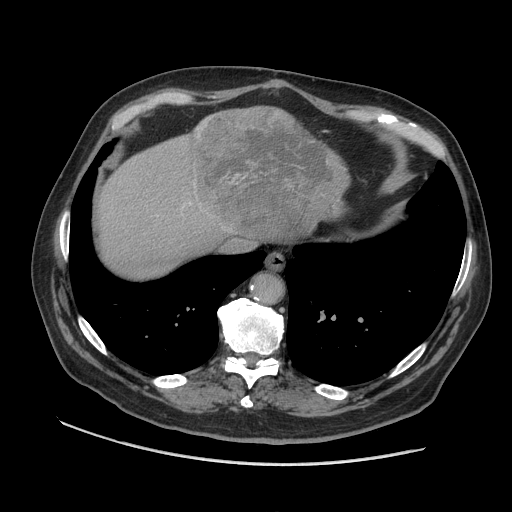
Contrast-enhanced abdominal CT (liver protocol), one axial slice. Position 86 of 109 along the scan axis. Reconstruction kernel STANDARD. 140 kVp. Soft-tissue window (W 400 / L 40 HU). 2.5 mm slice thickness. 512 × 512 image matrix, field of view 420 × 420 mm. Case-level facts recorded for this patient, not image findings: diagnosis: hepatocellular carcinoma (patient treated with transarterial chemoembolisation; whether this scan precedes or follows treatment is not stated here); TNM stage (as recorded): Stage-I; Child-Pugh class: A; tumour nodularity: uninodular.
Outlined on this slice (semi-automatically segmented with operator editing):
- liver parenchyma outside the tumour (the mass and vessels are separate outlines, so this box may not span the whole liver): bounding box (x1, y1, x2, y2) in pixels: (98, 110, 274, 278)
- mass: (191, 105, 349, 239)